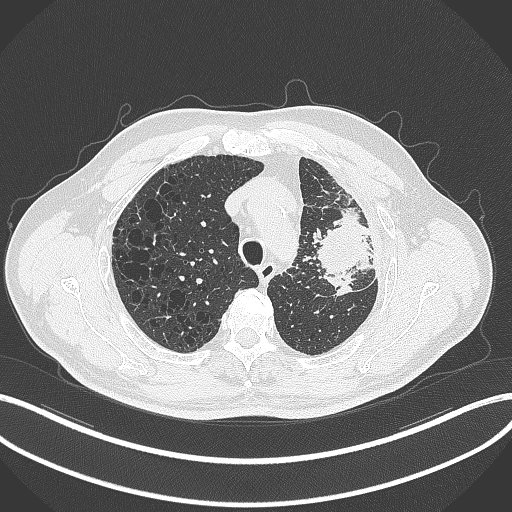
Chest CT, one axial slice. Position 249 of 297 along the scan axis. 120 kVp. Lung window (W 1500 / L -600 HU). 1 mm slice thickness. 512 × 512 image matrix. Patient: male, 68 years. From the clinical record (not read from this slice): clinical TNM (as recorded): T3 N3 M1.
Outlined on this slice (rectangle marked by the reading radiologist):
- lung tumour (recorded histology: adenocarcinoma): bounding box [x1, y1, x2, y2] px = [312, 198, 372, 300]